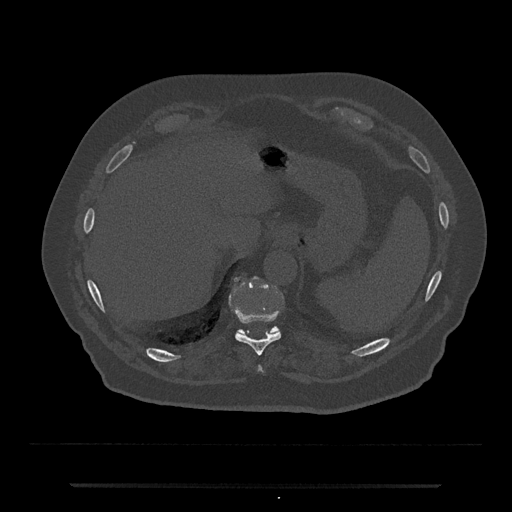
CT including the spine, one axial slice; slice 692 of 797 in the series (ordered by position); reconstruction kernel Br40s/3; bone window (W 1800 / L 400 HU); 0.5 mm slice thickness; 512 × 512 image matrix. Male patient, age 80 years. From the clinical record (not read from this slice): primary cancer: prostate; vertebrae with lytic lesions (as recorded): L1, T11.
Structures marked on this image (semi-automatic segmentation, software-assisted and operator-edited):
- T10 vertebra: bounding box (x1, y1, x2, y2) in pixels: (235, 278, 281, 356)
- T11 vertebra: (237, 277, 280, 333)
- T9 vertebra: (259, 367, 261, 371)